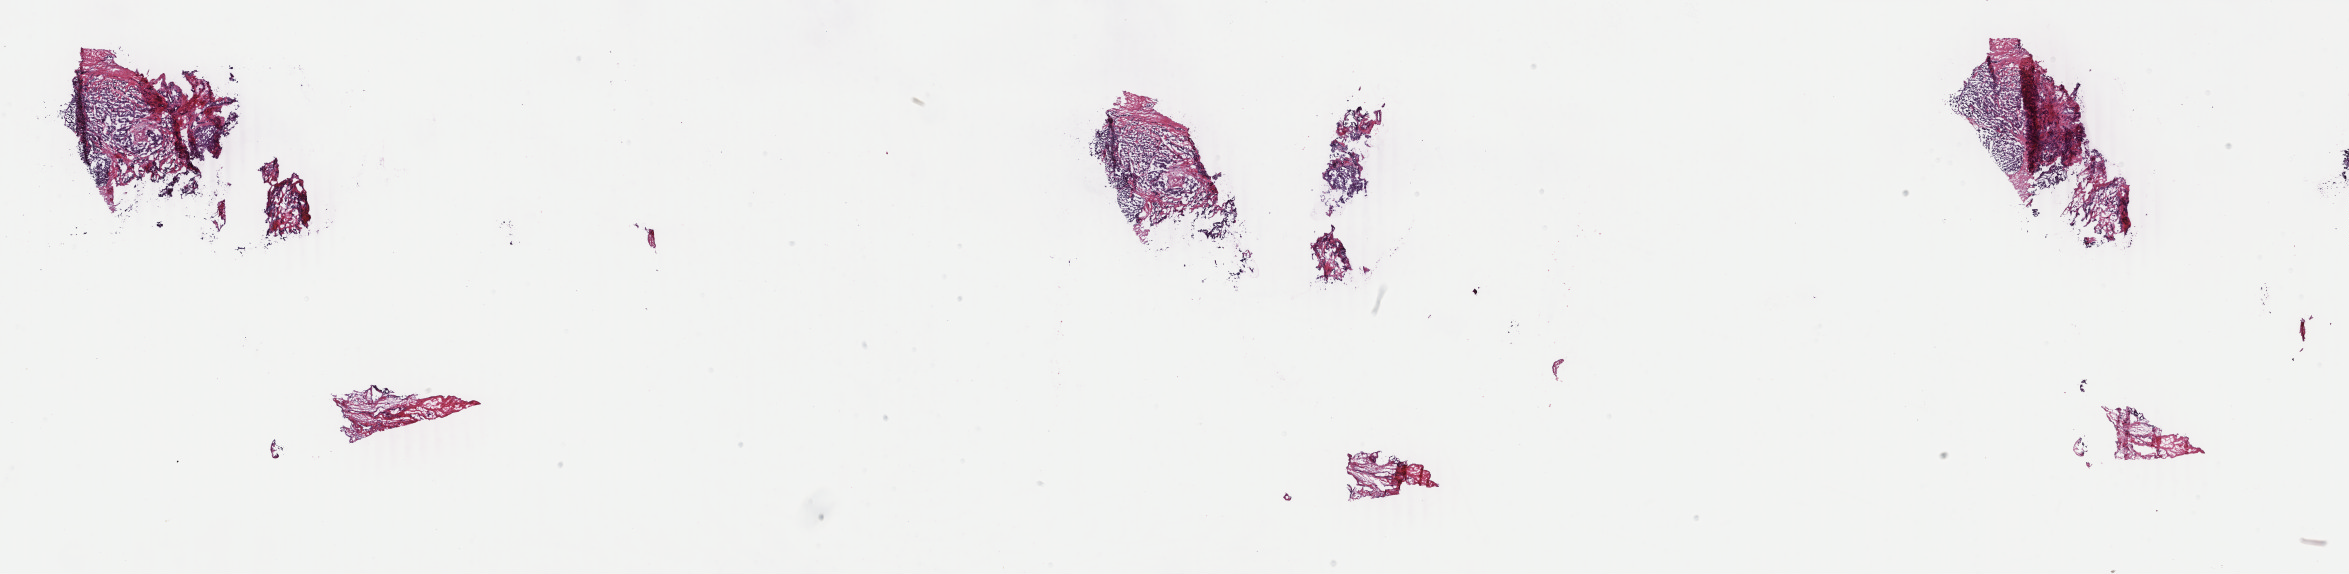
H&E whole-slide image, shown as a low-resolution overview of the whole scanned area (about 37.4 x 9.1 mm). Frozen section. Breast, primary tumour sample. Female patient; age at initial diagnosis 66 years. Composition of this section per pathologist review: tumour cells 90%, tumour nuclei 90%, normal cells 0%, stromal cells 10%, necrosis 0%. Inflammatory infiltration, as recorded: lymphocyte infiltration 1%, monocyte infiltration 0%, neutrophil infiltration 0%.
AJCC pathologic stage: IIA. Laterality: left. TNM: T2 N0 (i-) M0. Diagnosis: Infiltrating duct carcinoma, NOS. Lymph nodes positive (case pathology): 0 of 17 examined.